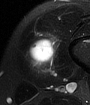
MRI of an extremity soft-tissue mass, one axial slice; position 15 of 65 along the scan axis; T2-weighted fat-saturated; MR volume resampled by the dataset authors to the PET/CT grid (not the native acquisition matrix); 90 × 105 image matrix. Male patient. From the clinical record (not read from this slice): histological type: mixoid liposarcoma; grade: low; site of the primary tumour: left thigh.
Structures marked on this image (expert contour drawn on MRI and transferred to this co-registered scan by the dataset authors):
- gross tumour volume (mass): bounding box [x1, y1, x2, y2] px = [29, 37, 53, 63]